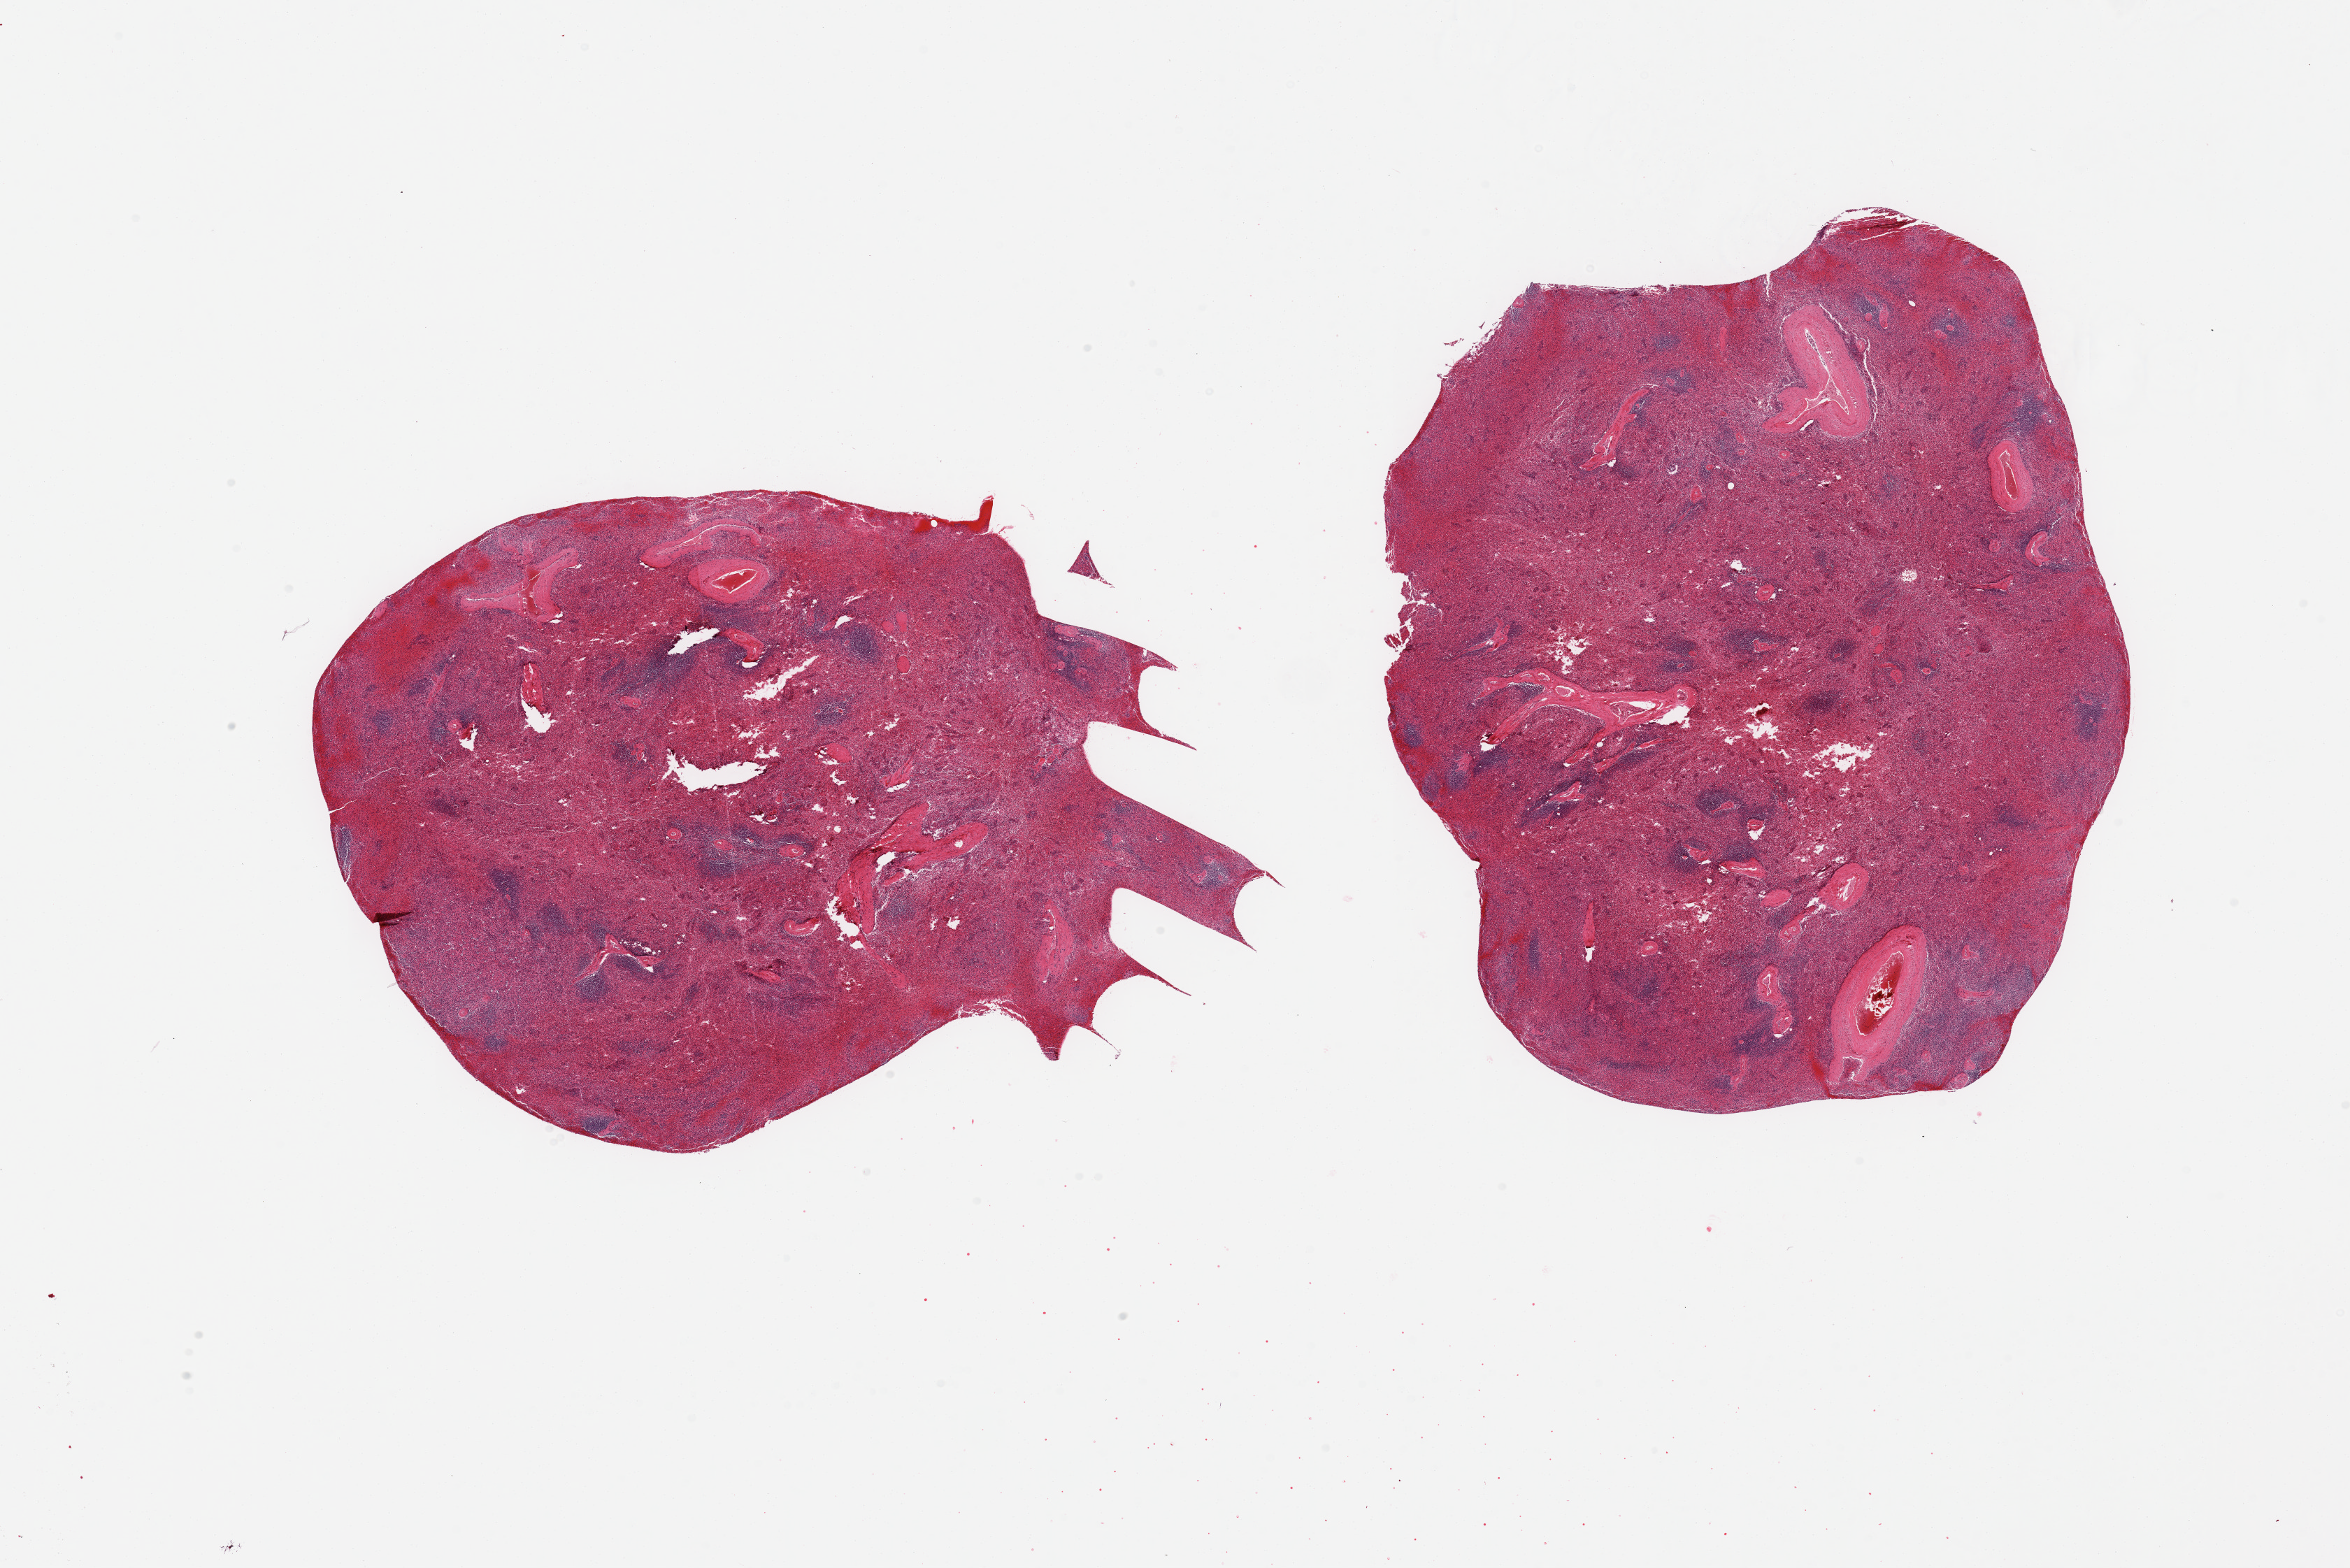
Whole-slide image, H&E stain, shown as a low-resolution overview of the whole scanned area (about 26.6 x 17.7 mm, from a 20x scan). PAXgene-fixed paraffin-embedded (PFPE) section. Sampled site (target tissue): spleen. Donor tissue sample. Donor sex: male.
Reviewer comment on this tissue sample: 2 pieces; congestion.